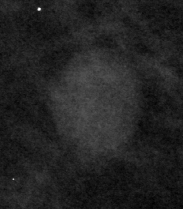
Crop from a digitized film mammogram around one marked abnormality; left breast; MLO view.
Marked abnormality: mass, shape lymph node, margins circumscribed; BI-RADS assessment category 2; benign without callback (not worked up further).